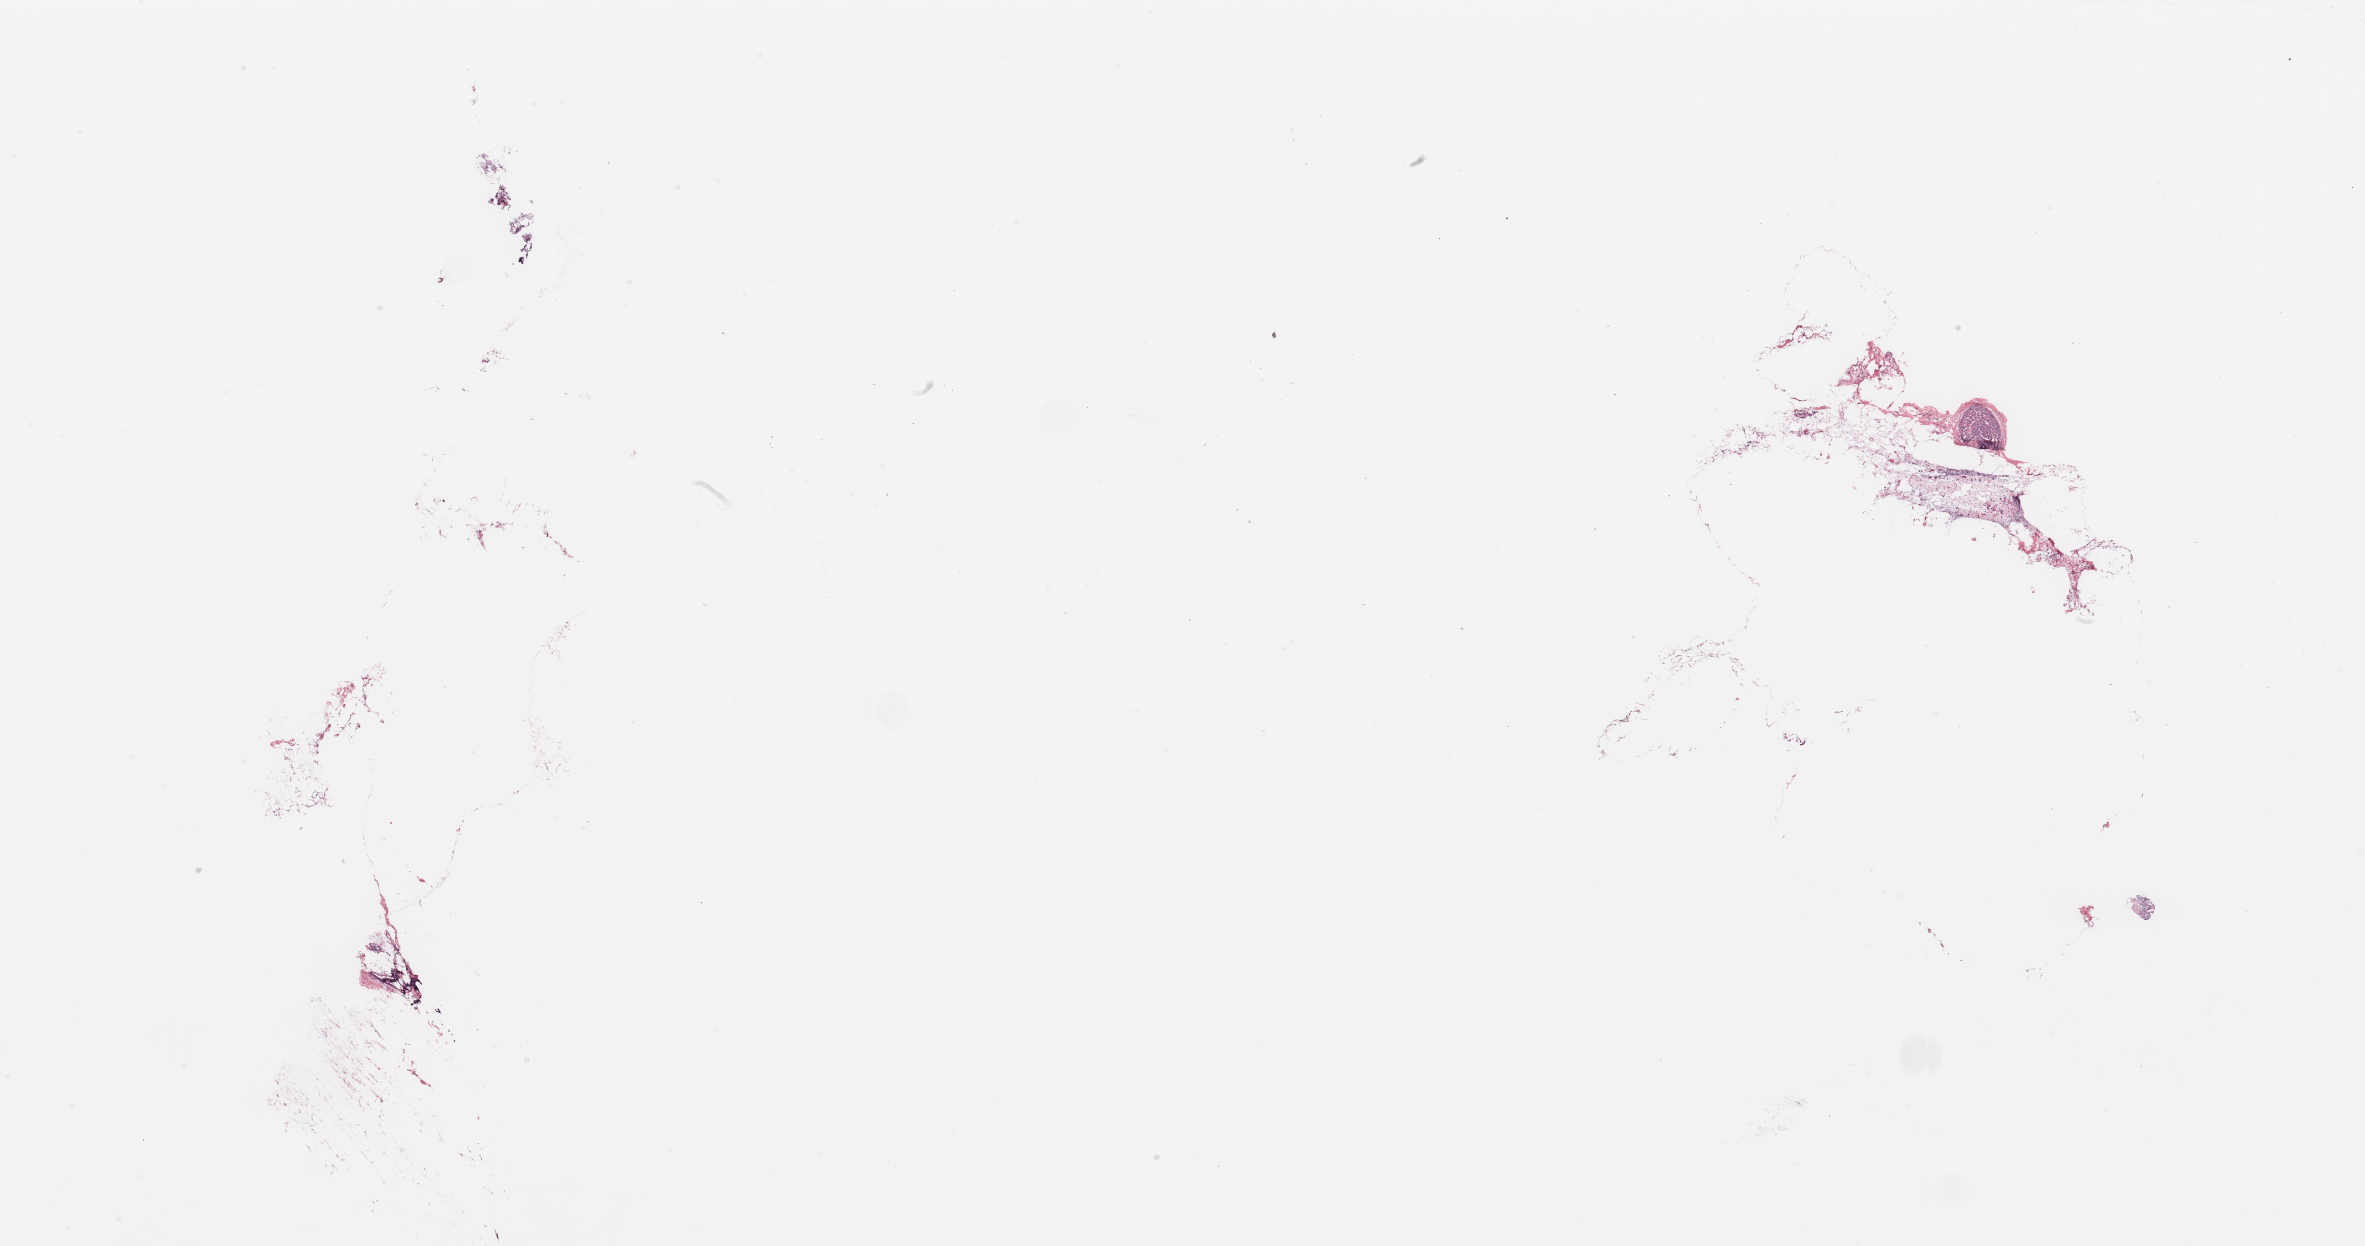
Digitized Hematoxylin and eosin (H&E) stained tissue section (whole slide), whole scanned area (about 37.4 x 19.7 mm, from a 20x scan) shown as a low-resolution overview; breast, tumour tissue. Female, 62 y/o.
Diagnosis: Infiltrating duct carcinoma, NOS.